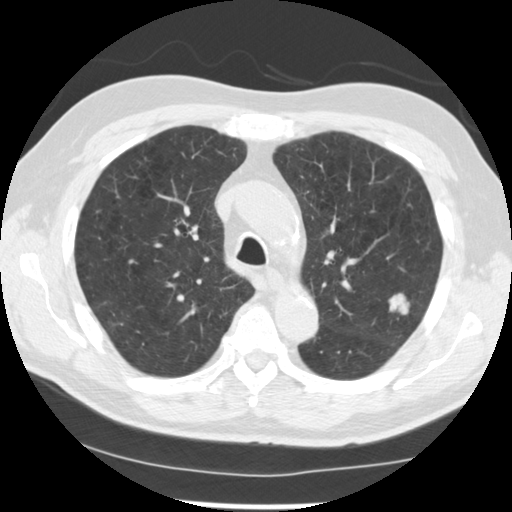
Low-dose screening chest CT, one axial slice. Position 174 of 249 along the scan axis. Reconstruction kernel STANDARD. 120 kVp. Lung window (W 1500 / L -600 HU). 512 × 512 image matrix, field of view 341 × 341 mm.
Annotated regions visible in this slice (manually delineated by an expert):
- lesion 1 (tumor, upper lobe of left lung): bounding box <389,293,409,315> (left, top, right, bottom; pixels)